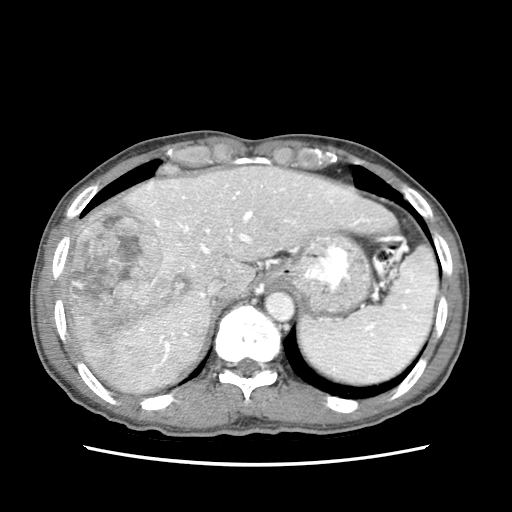
Contrast-enhanced abdominal CT (liver protocol), one axial slice; position 56 of 79 along the scan axis; reconstruction kernel STANDARD; soft-tissue window (W 400 / L 40 HU); 2.5 mm slice thickness; 512 × 512 image matrix. From the clinical record (not read from this slice): diagnosis: hepatocellular carcinoma (patient treated with transarterial chemoembolisation; whether this scan precedes or follows treatment is not stated here); TNM stage (as recorded): Stage-IIIB; Child-Pugh class: A; tumour differentiation: moderately differentiated.
Outlined on this slice (semi-automatically segmented with operator editing):
- abdominal aorta: bounding box <265,292,293,321> (left, top, right, bottom; pixels)
- liver parenchyma outside the tumour (the mass and vessels are separate outlines, so this box may not span the whole liver): <59,164,396,394>
- mass: <63,191,197,358>
- liver vessels: <137,178,334,361>